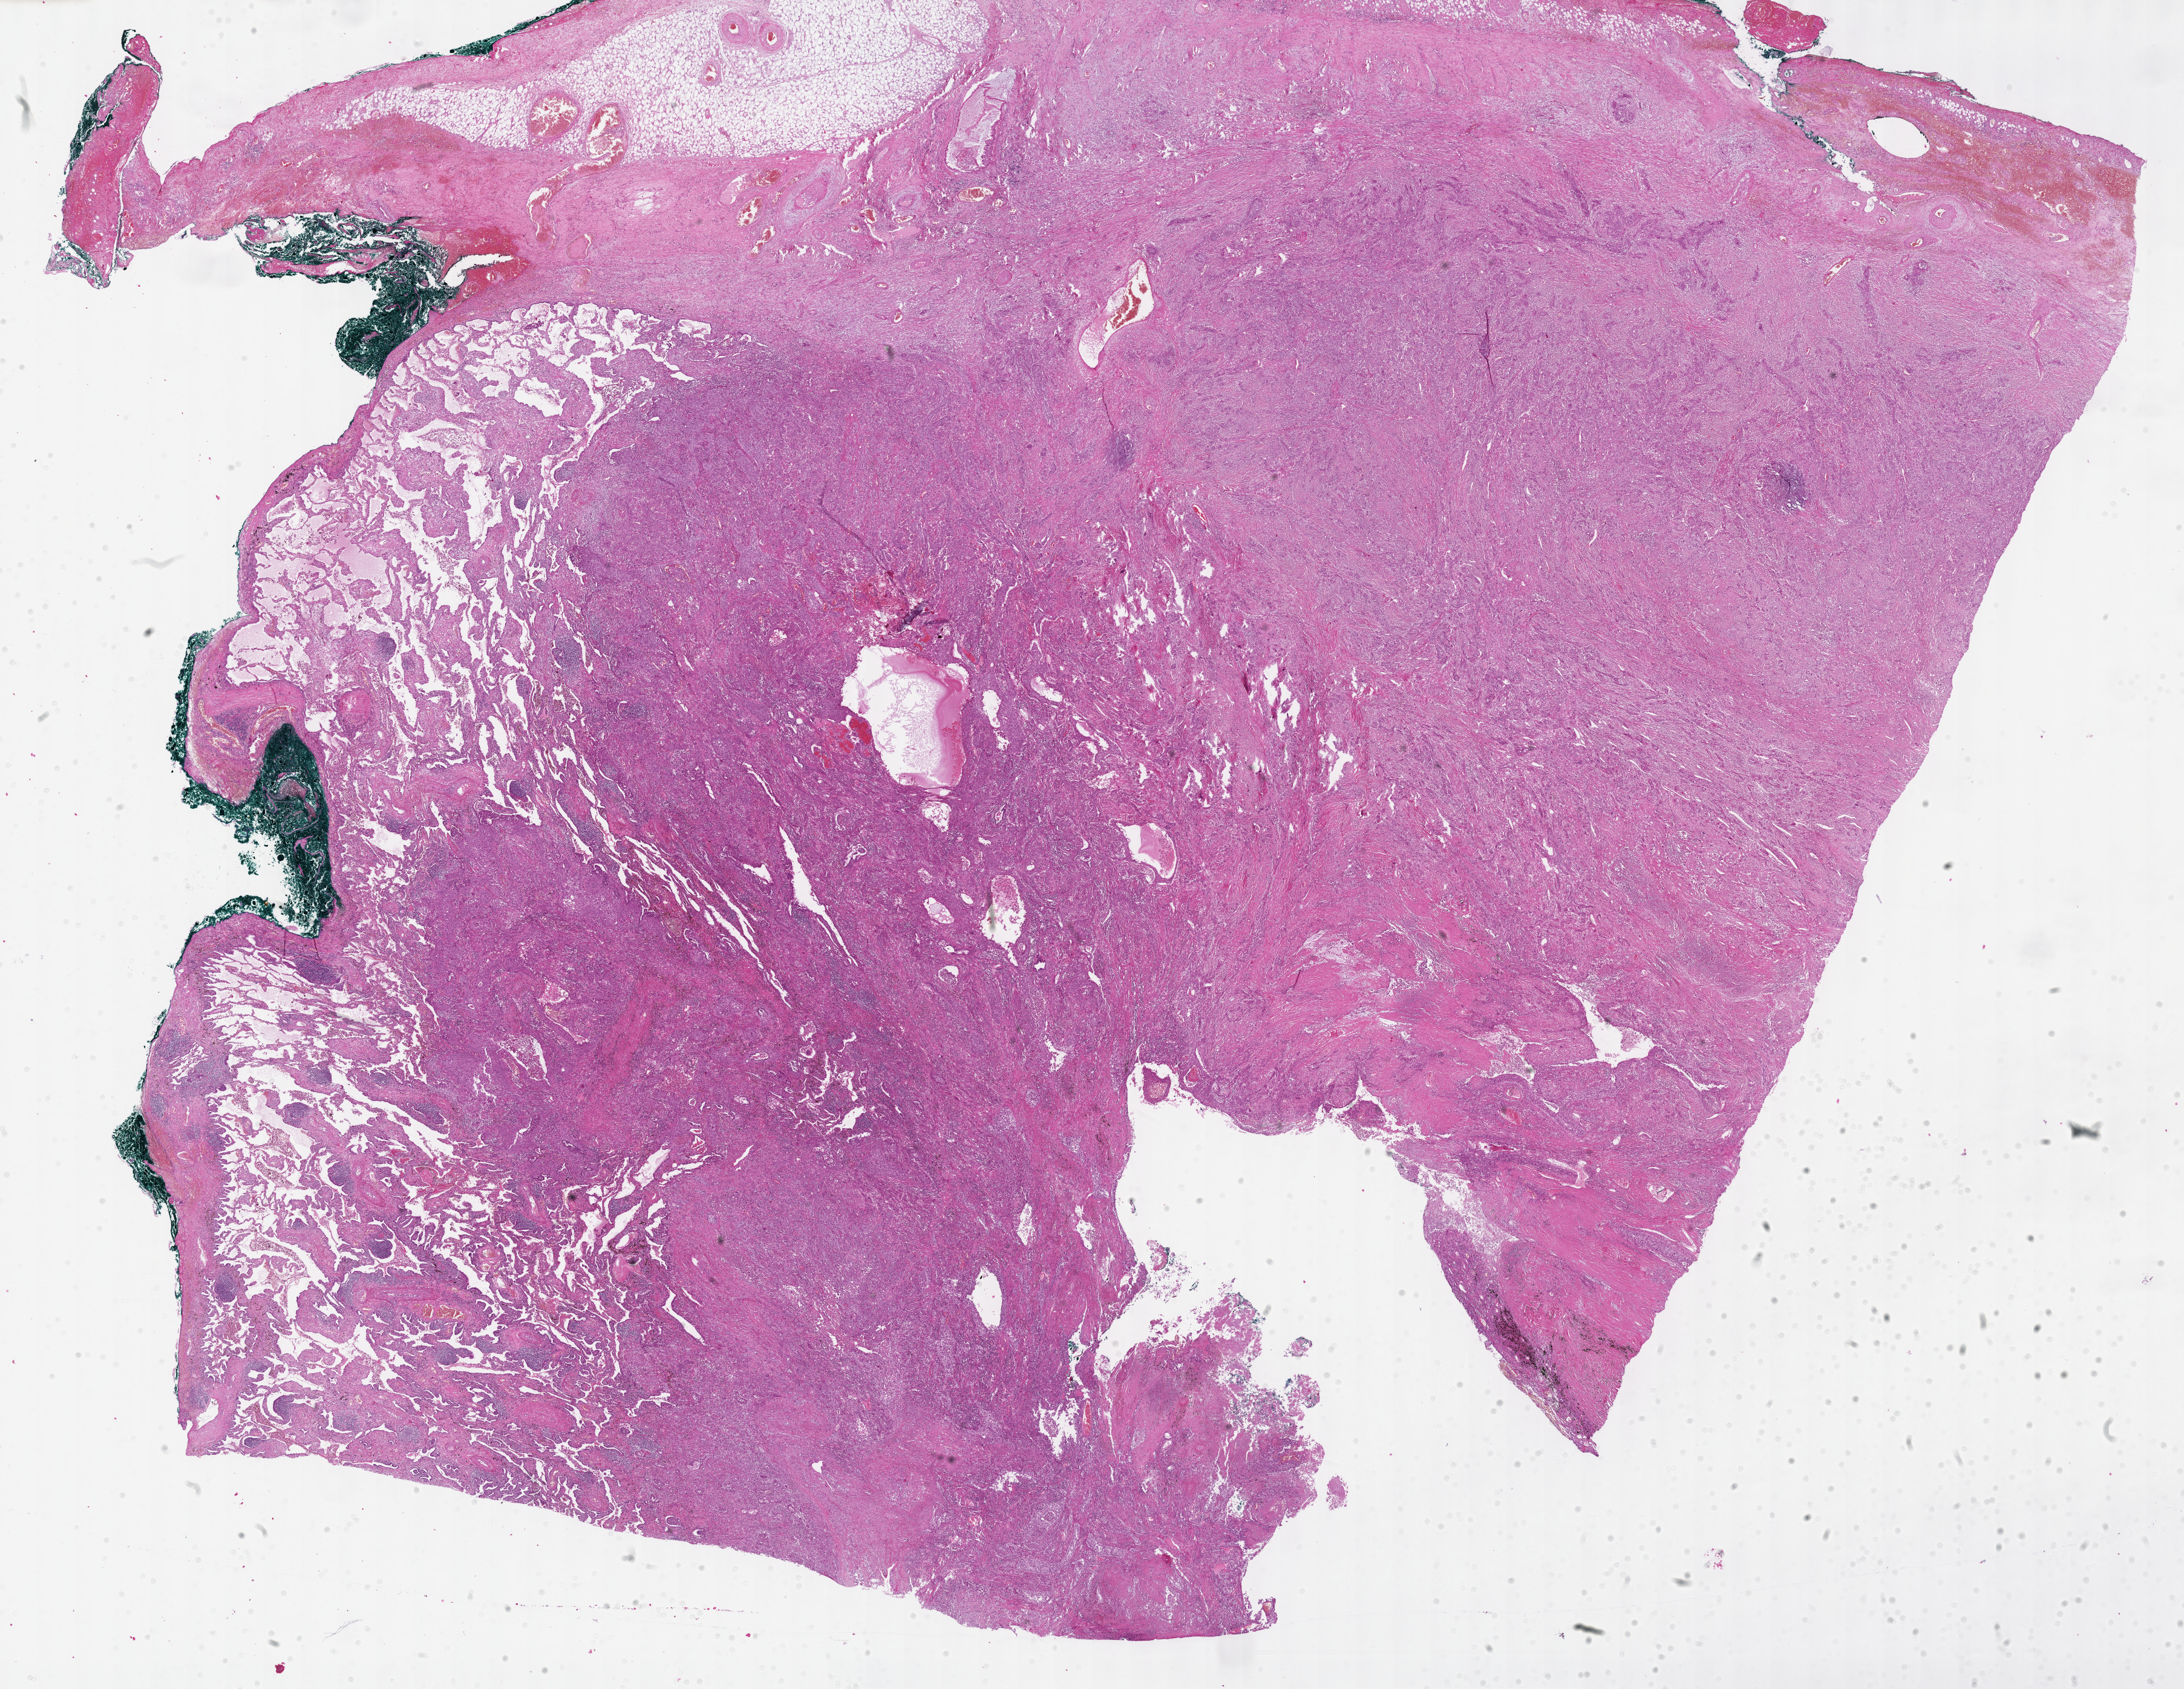
Digitized H&E-stained tissue section (whole slide) — low-resolution overview of the scanned area, about 29.2 x 22.6 mm (acquisition: 40x scan). Formalin-fixed paraffin-embedded (FFPE) diagnostic section. Lung, primary tumour sample. Female patient; age at initial diagnosis 58 years.
- AJCC pathologic stage: IIB
- histologic diagnosis: Squamous cell carcinoma, NOS (overlapping lesion of lung)
- laterality: left